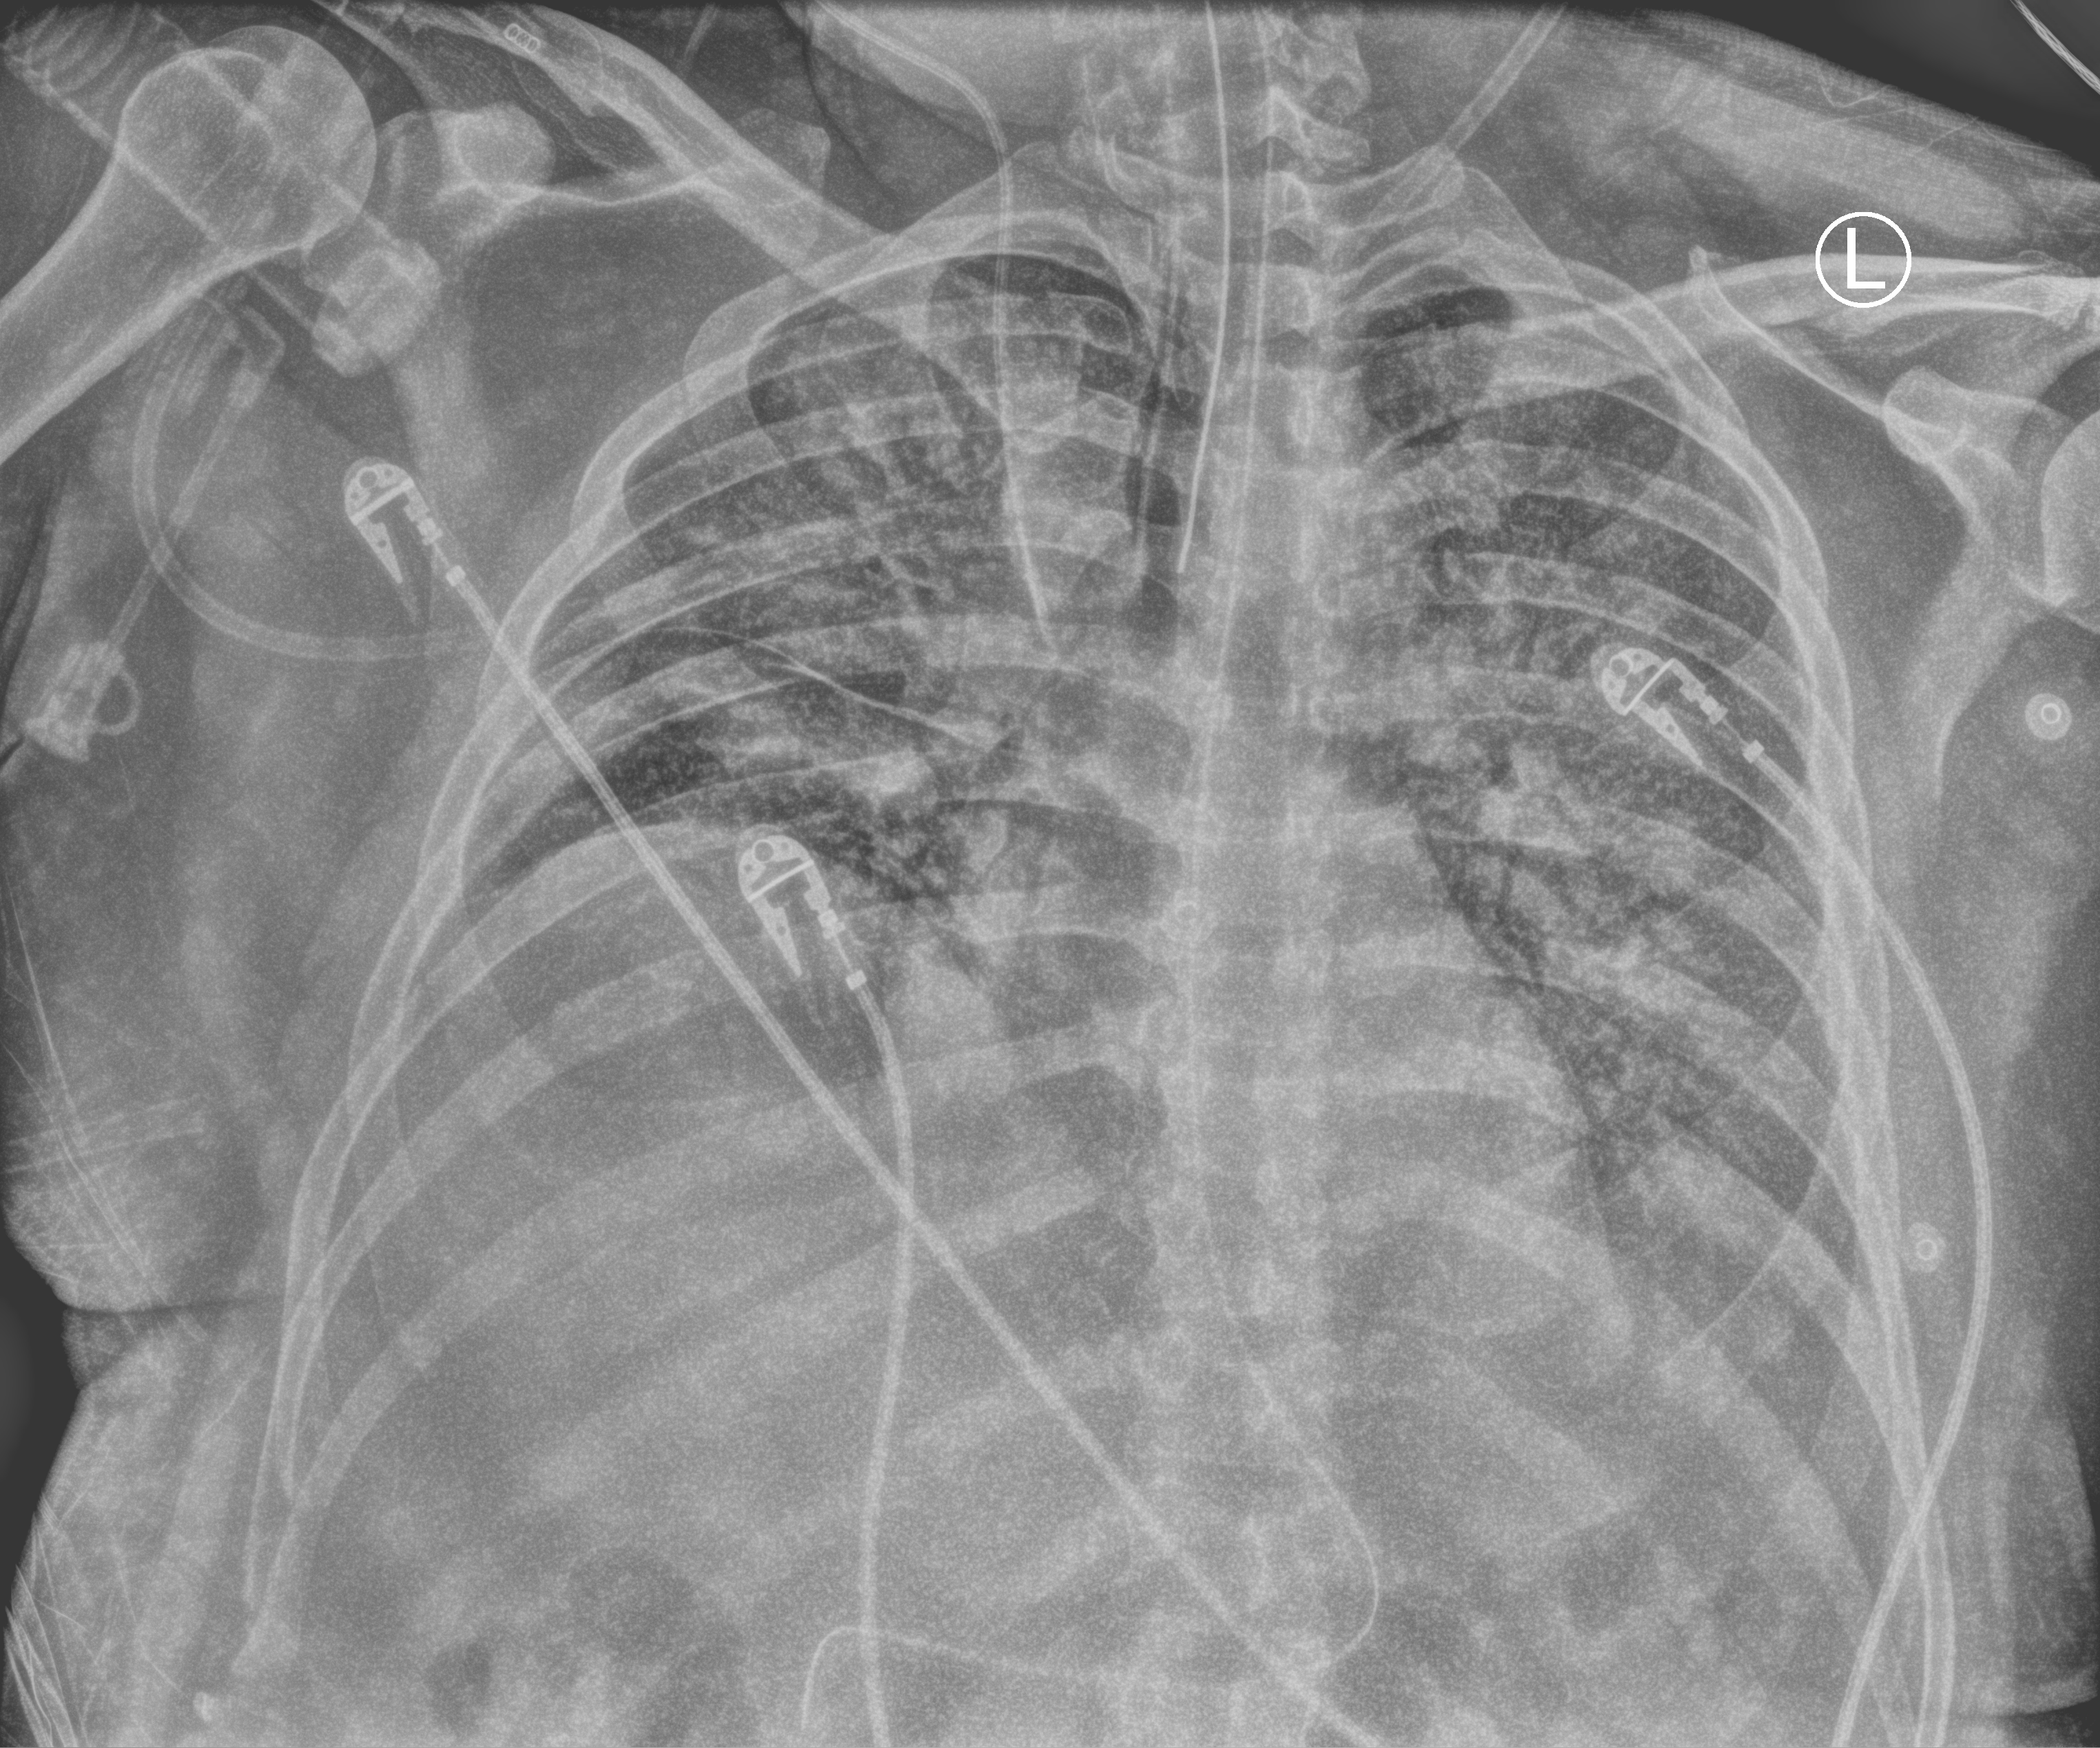
Portable chest radiograph, anteroposterior (AP) projection. Patient hospitalised with COVID-19; male, aged 18–59 years.
Hospital-stay facts (about this admission, not read from this image; timing relative to this image not recorded): COPD (admission record): no; admitted to intensive care during this hospital stay: yes.